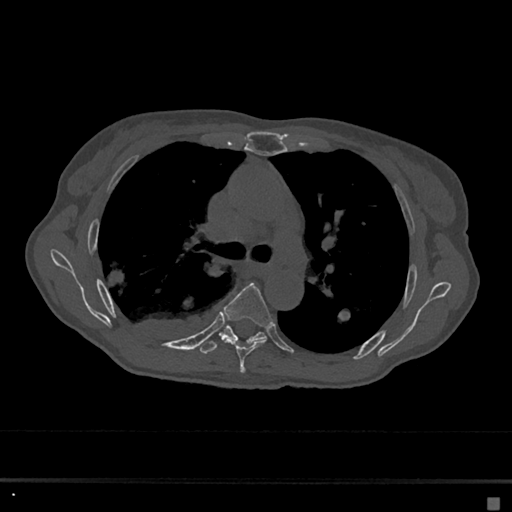
CT including the spine, one axial slice. Slice 446 of 797 in the series (ordered by position). Reconstruction kernel Br40s/3. 120 kVp. Bone window (W 1800 / L 400 HU). 0.5 mm slice thickness. 512 × 512 image matrix. Patient: female, 68 years. Case-level facts recorded for this patient, not image findings: primary cancer: renal.
Annotated regions visible in this slice (semi-automatic segmentation, software-assisted and operator-edited):
- T5 vertebra: box from (x=224, y=283) to (x=272, y=373) px
- T6 vertebra: (x=199, y=325)–(x=266, y=354)